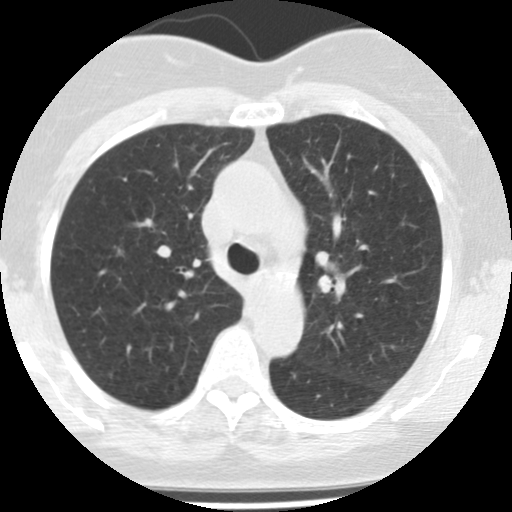
Axial slice from a low-dose chest CT screening exam. Baseline annual screen. Lung window (W 1500 / L -600 HU). 2.5 mm slice thickness. 120 kVp. 512 × 512 image matrix. Female participant, aged 62 years at enrolment. Former smoker at enrolment.
Expert reader's lesion annotation, bounding box (x1, y1, x2, y2) in pixels: (91, 235, 138, 272). Screening reader's record for this exam: no non-calcified nodule ≥4 mm recorded. Official screen result: negative screen, minor abnormalities not suspicious for lung cancer.